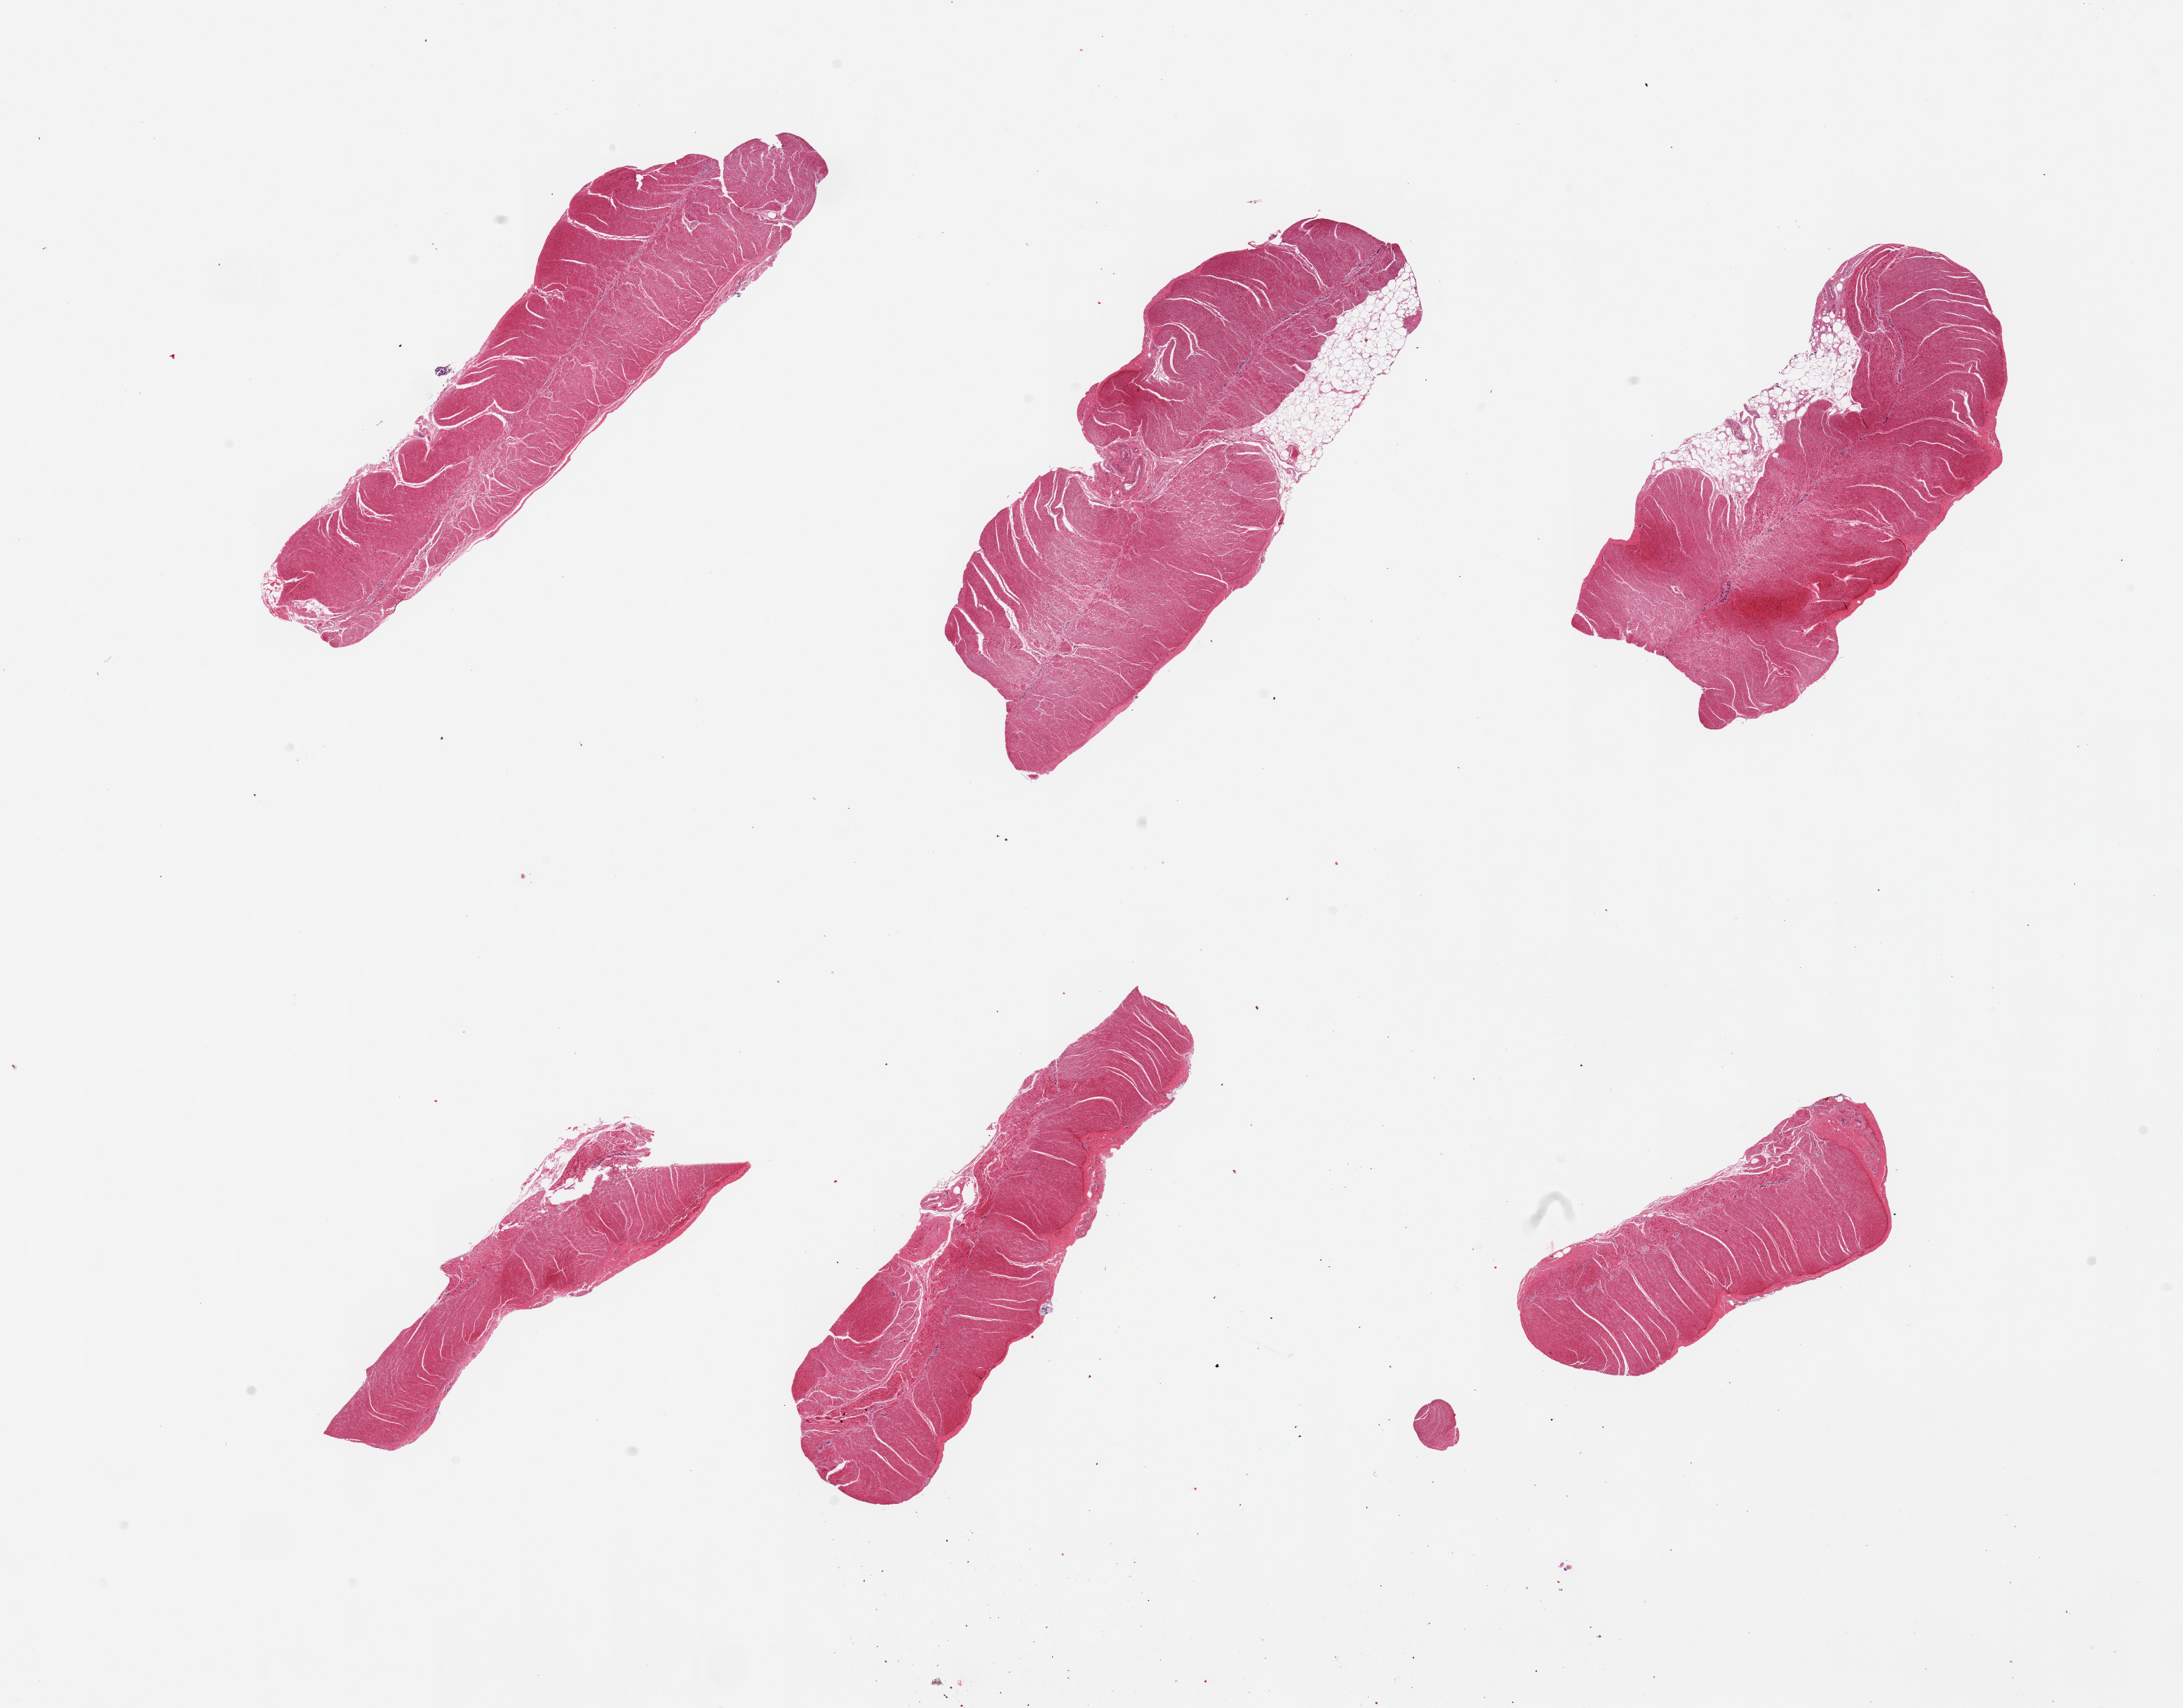
Digitized H&E-stained section, a low-resolution overview of the entire scanned area, about 24.6 x 19.3 mm (from a 20x scan), PAXgene-fixed, paraffin-embedded tissue, section of sigmoid colon (target tissue), donor tissue sample. Donor: female.
- reviewer comment on this tissue sample: 6 pieces; two pieces with about 10% adherent fat